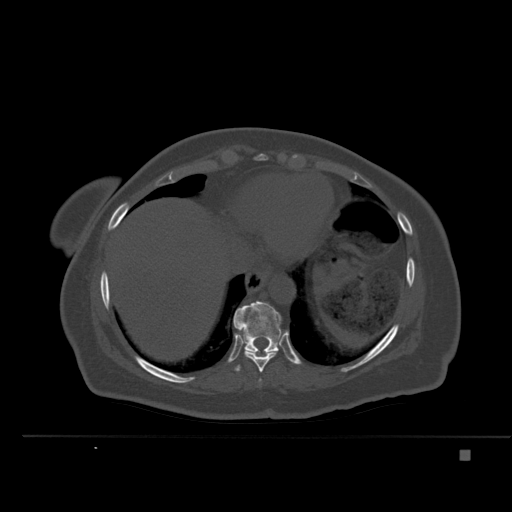
CT including the spine, one axial slice; slice 291 of 477 in the series (ordered by position); bone window (W 1800 / L 400 HU); 1.5 mm slice thickness; 512 × 512 image matrix, field of view 422 × 422 mm. Patient: female, 74 years. From the clinical record (not read from this slice): primary cancer: colon.
Annotated regions visible in this slice (semi-automatic segmentation, software-assisted and operator-edited):
- T10 vertebra: bounding box <233,301,282,353> (left, top, right, bottom; pixels)
- T8 vertebra: <259,379,262,382>
- T9 vertebra: <235,326,279,373>